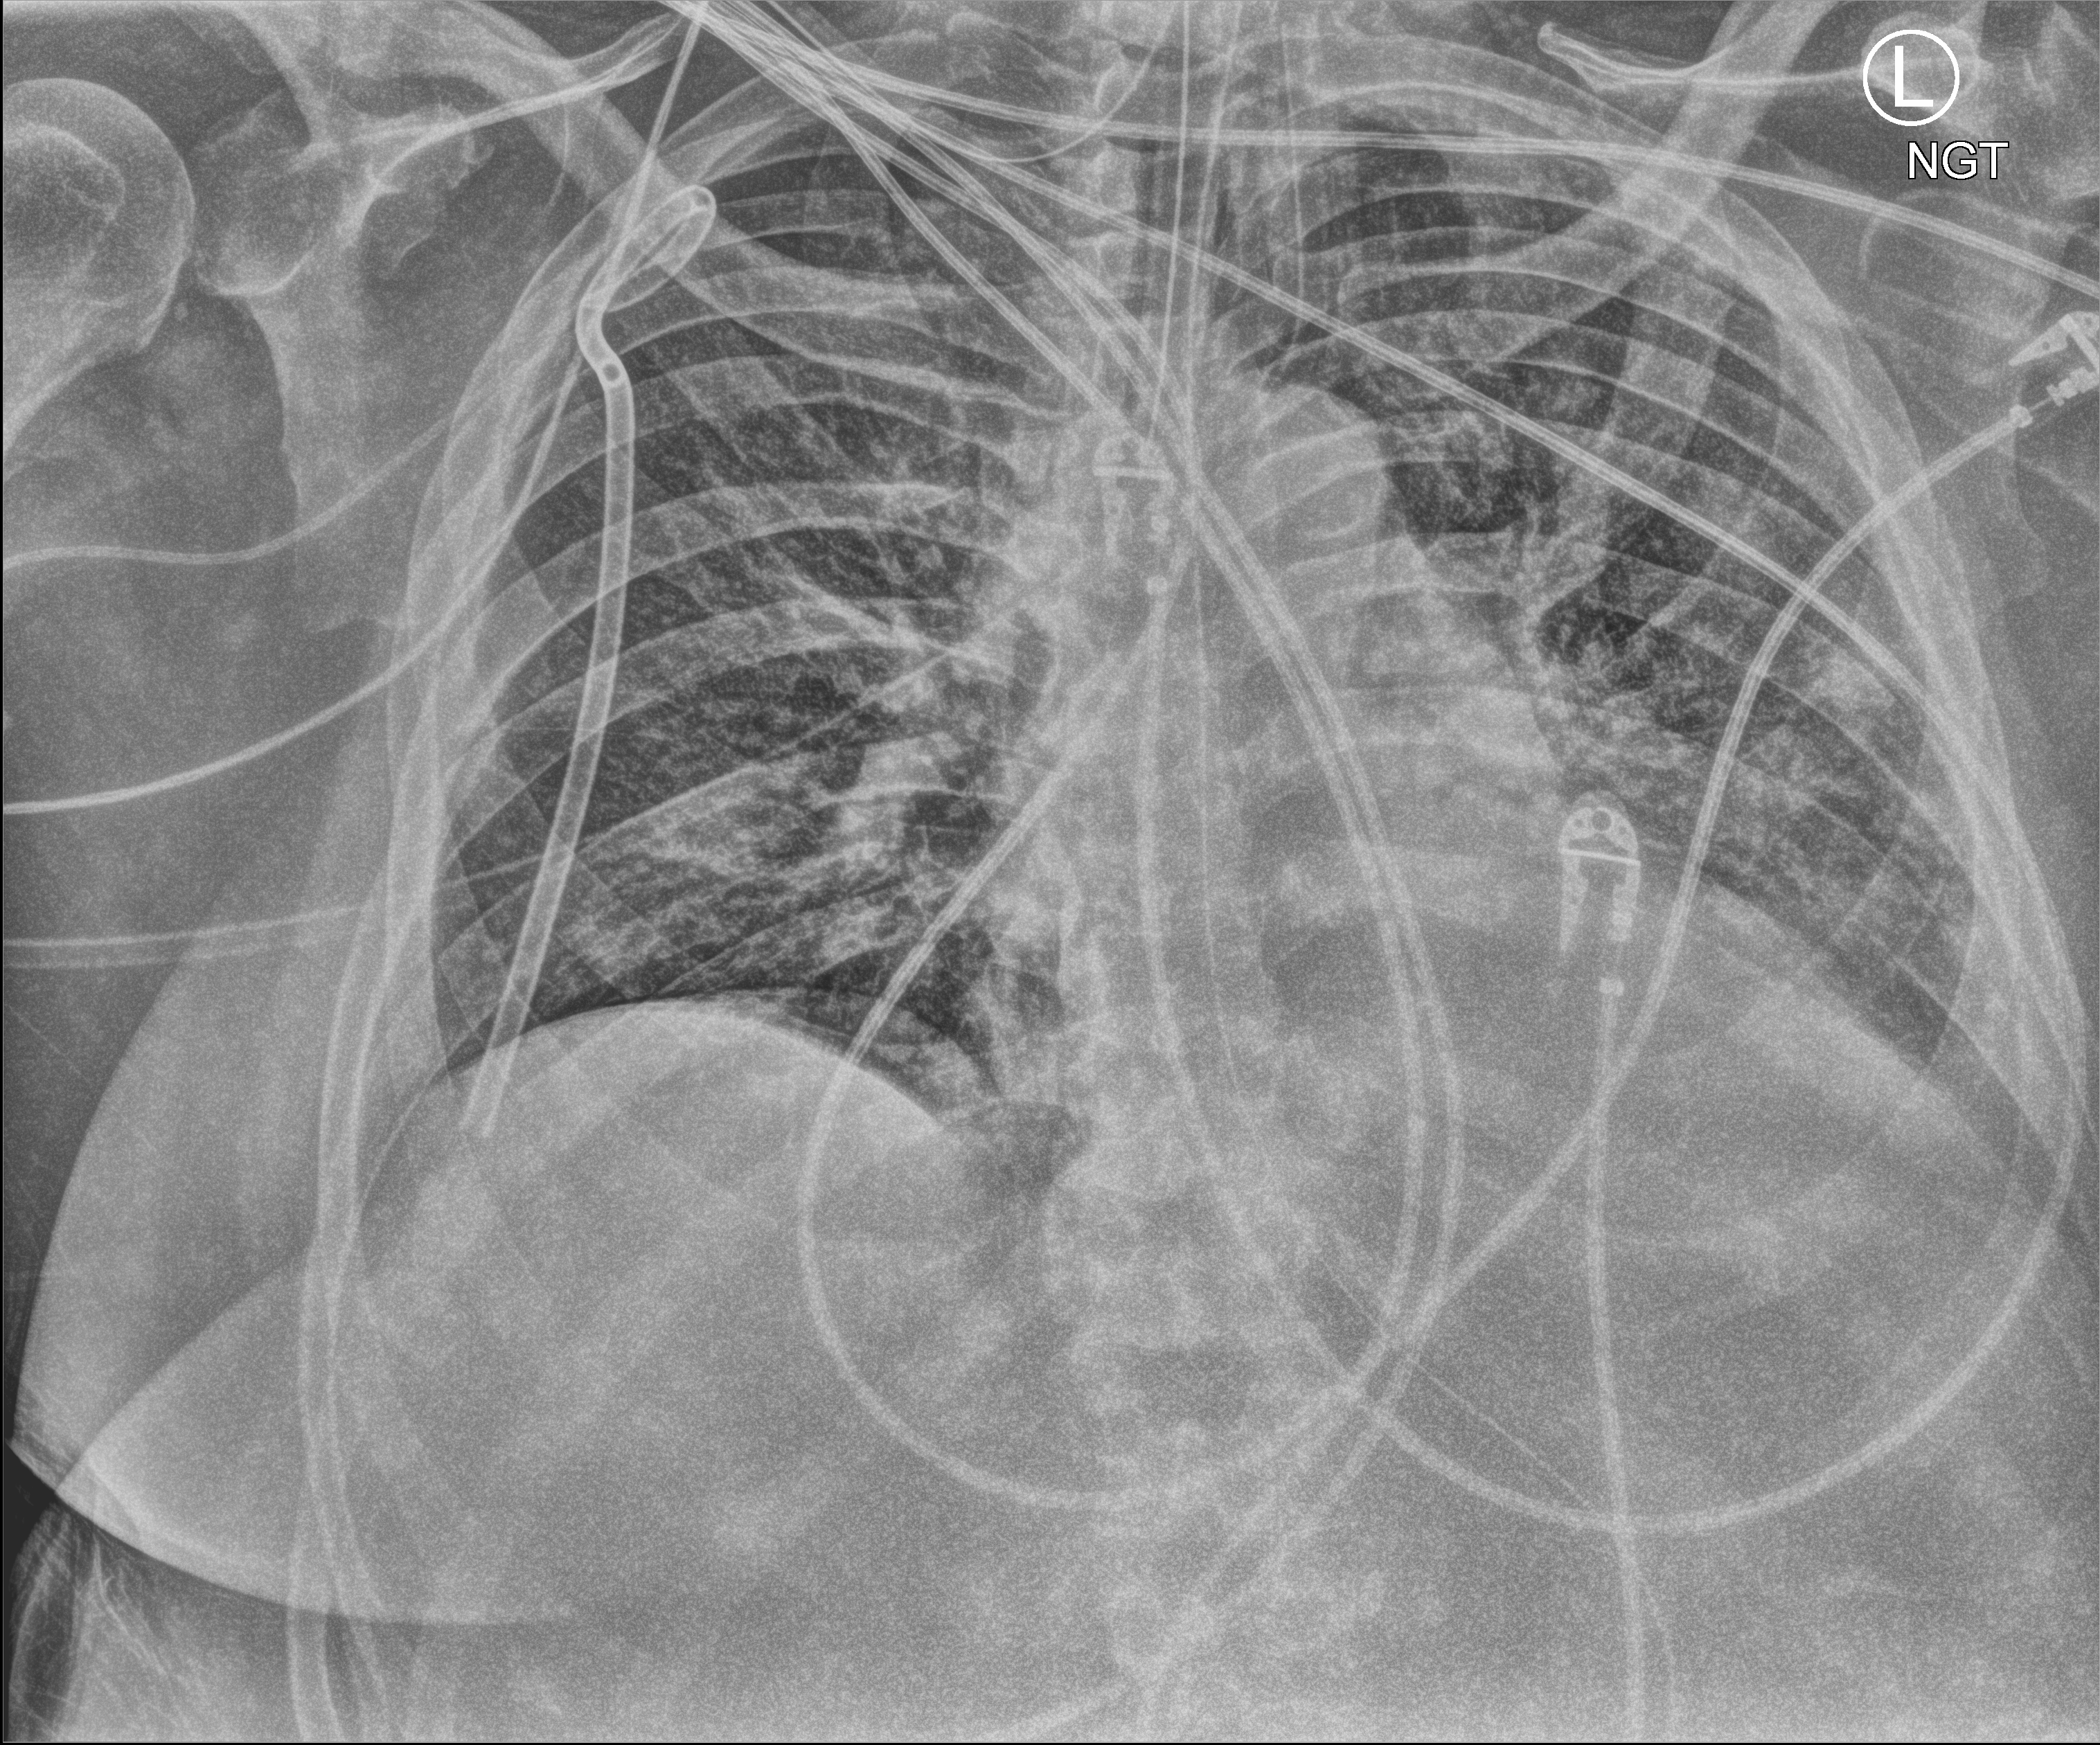
Portable chest radiograph, anteroposterior (AP) projection. Patient hospitalised with COVID-19; male, aged 60–74 years.
Admission-level facts for this patient (not findings on this image; timing relative to this image not recorded): mechanically ventilated during this hospital stay: yes; other chronic lung disease (admission record): no.